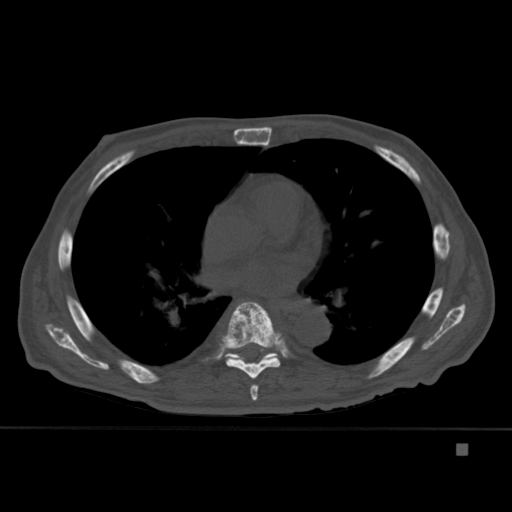
CT including the spine, one axial slice. Position 277 of 451 along the scan axis. Bone window (W 1800 / L 400 HU). 1.5 mm slice thickness. 512 × 512 image matrix, field of view 378 × 378 mm. Patient: male, 75 years. From the clinical record (not read from this slice): primary cancer: prostate.
Annotated regions visible in this slice (semi-automatic segmentation, software-assisted and operator-edited):
- T6 vertebra: bounding box (x1, y1, x2, y2) in pixels: (250, 384, 259, 401)
- T7 vertebra: (220, 302, 285, 379)
- T8 vertebra: (225, 353, 278, 362)